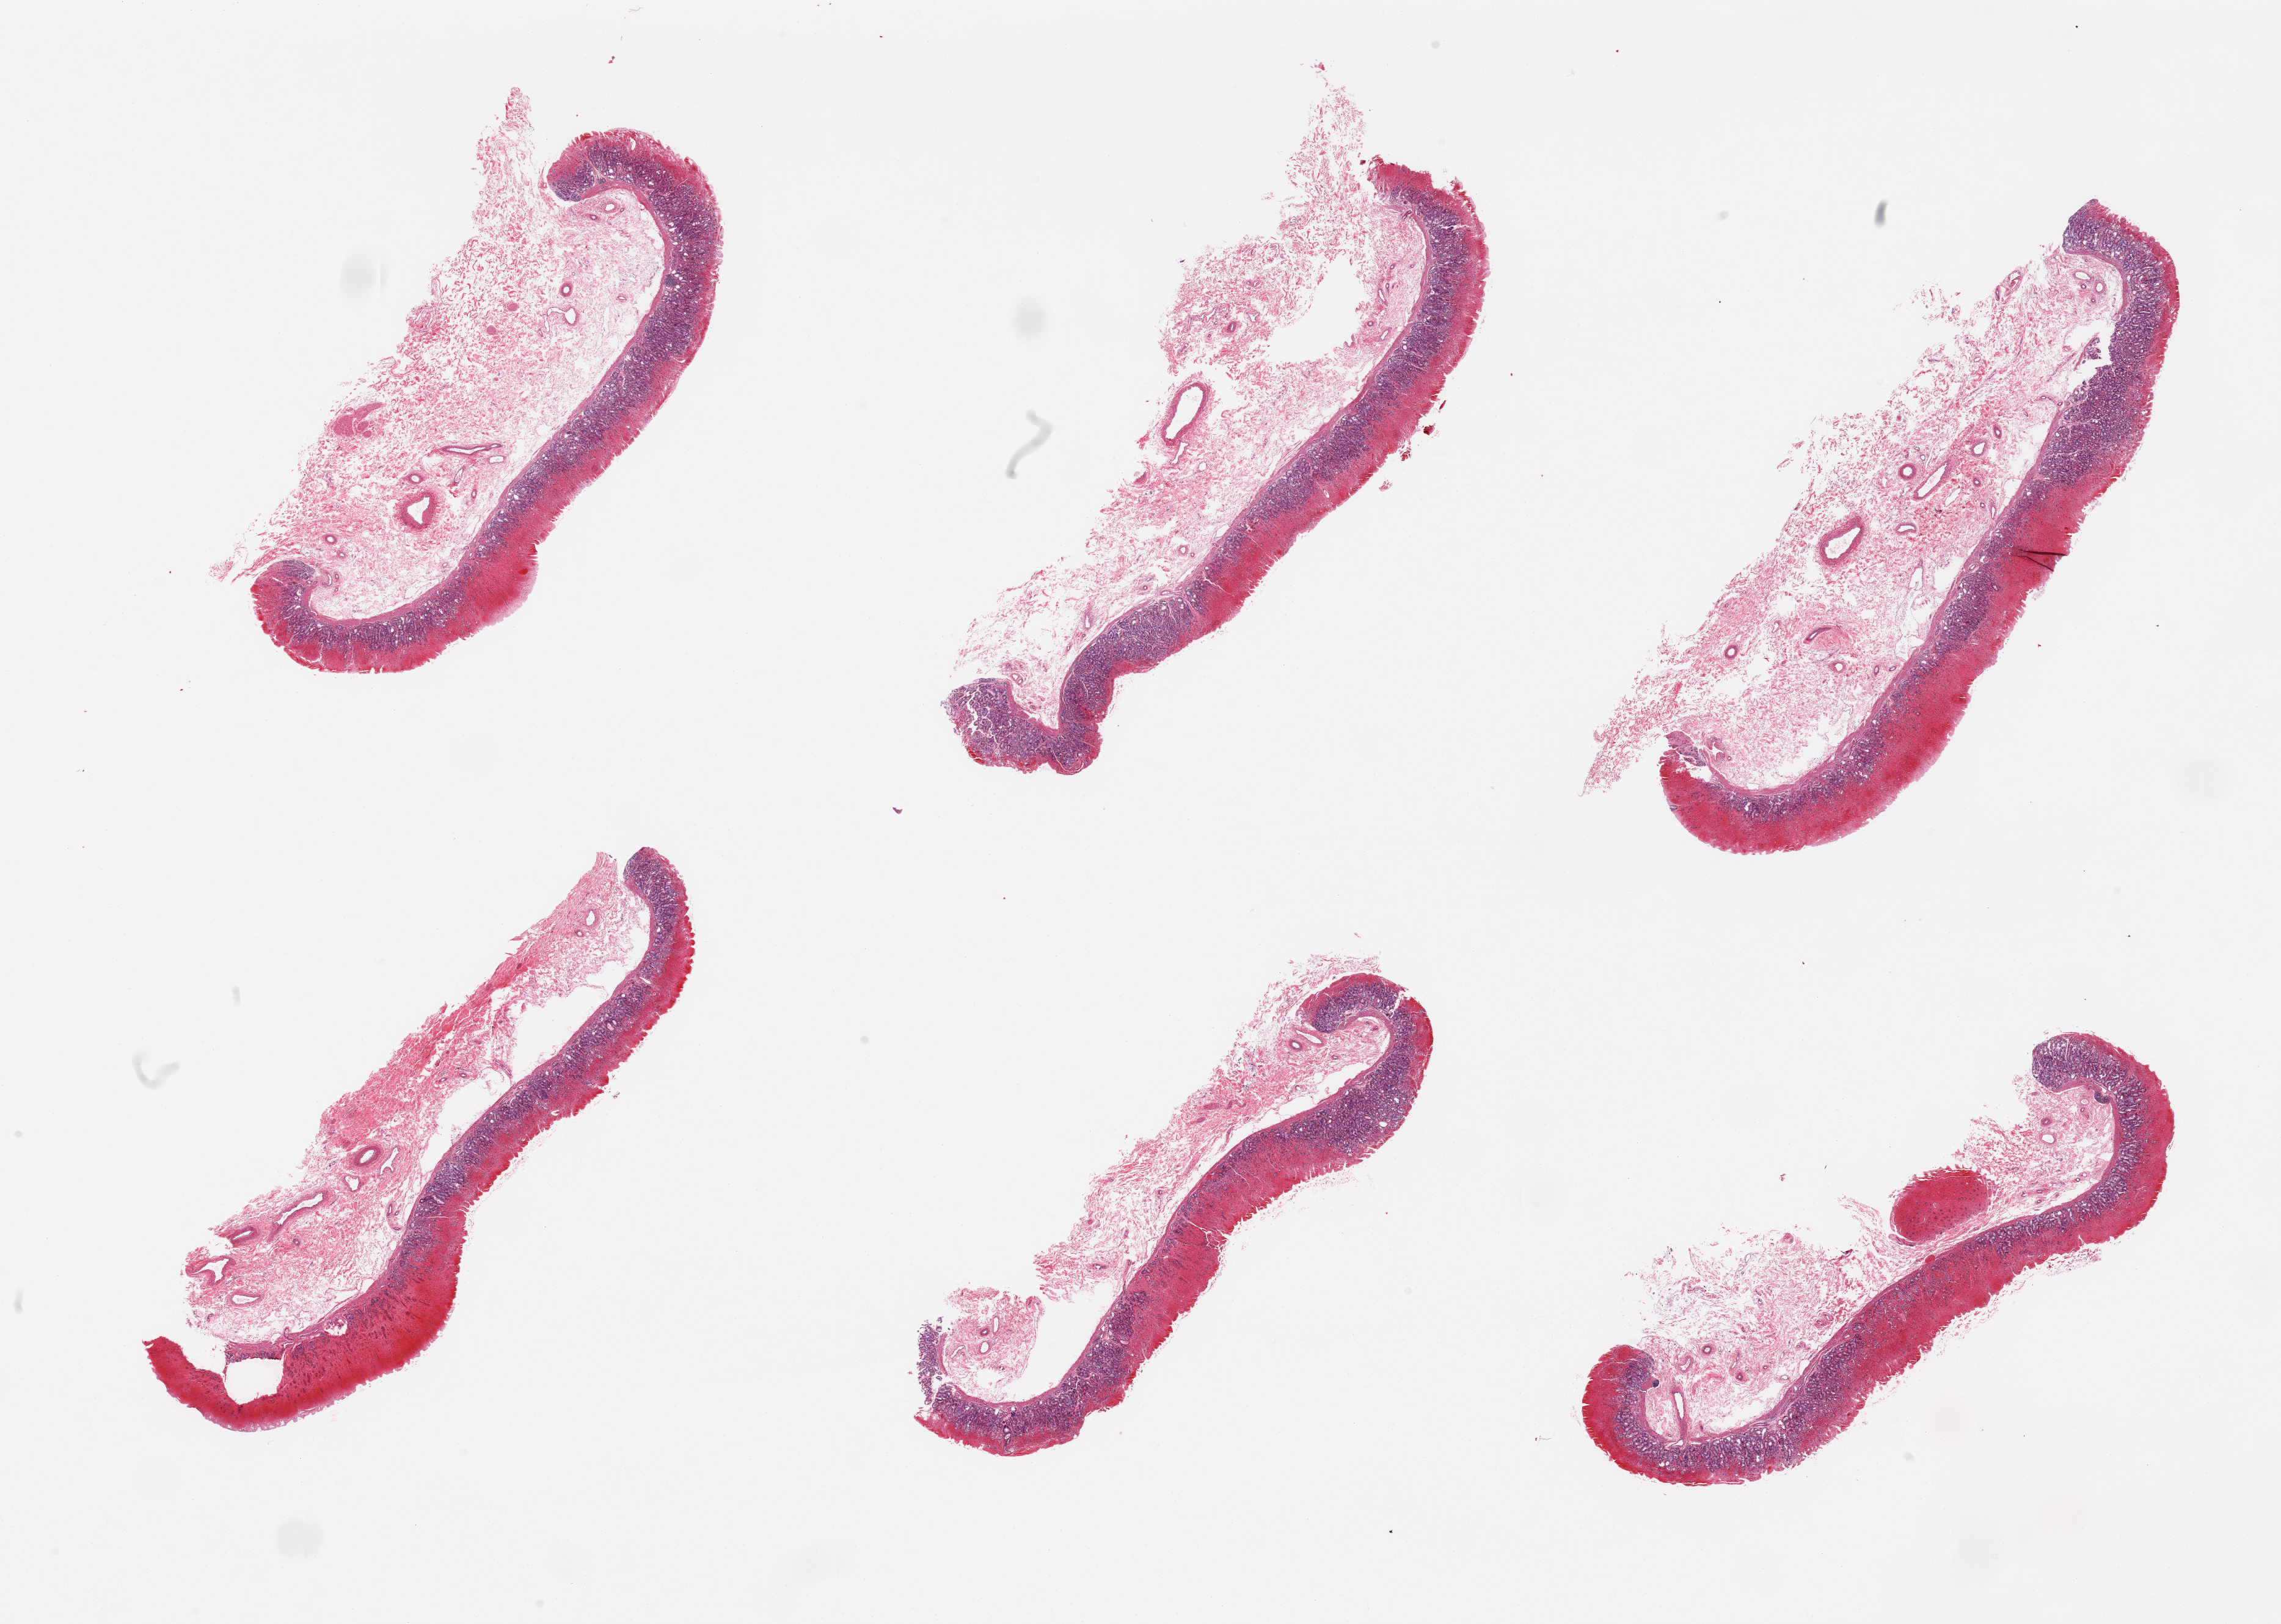
Digitized hematoxylin and eosin (H&E)-stained section, shown as a low-resolution overview of the whole scanned area (about 29.5 x 21.0 mm, acquisition: 20x scan). PAXgene-fixed, paraffin-embedded tissue. Section of stomach (target tissue). Donor tissue sample. Male donor.
Reviewer comment on this tissue sample: 6 pieces, acute hemorrhagic gastropathy.